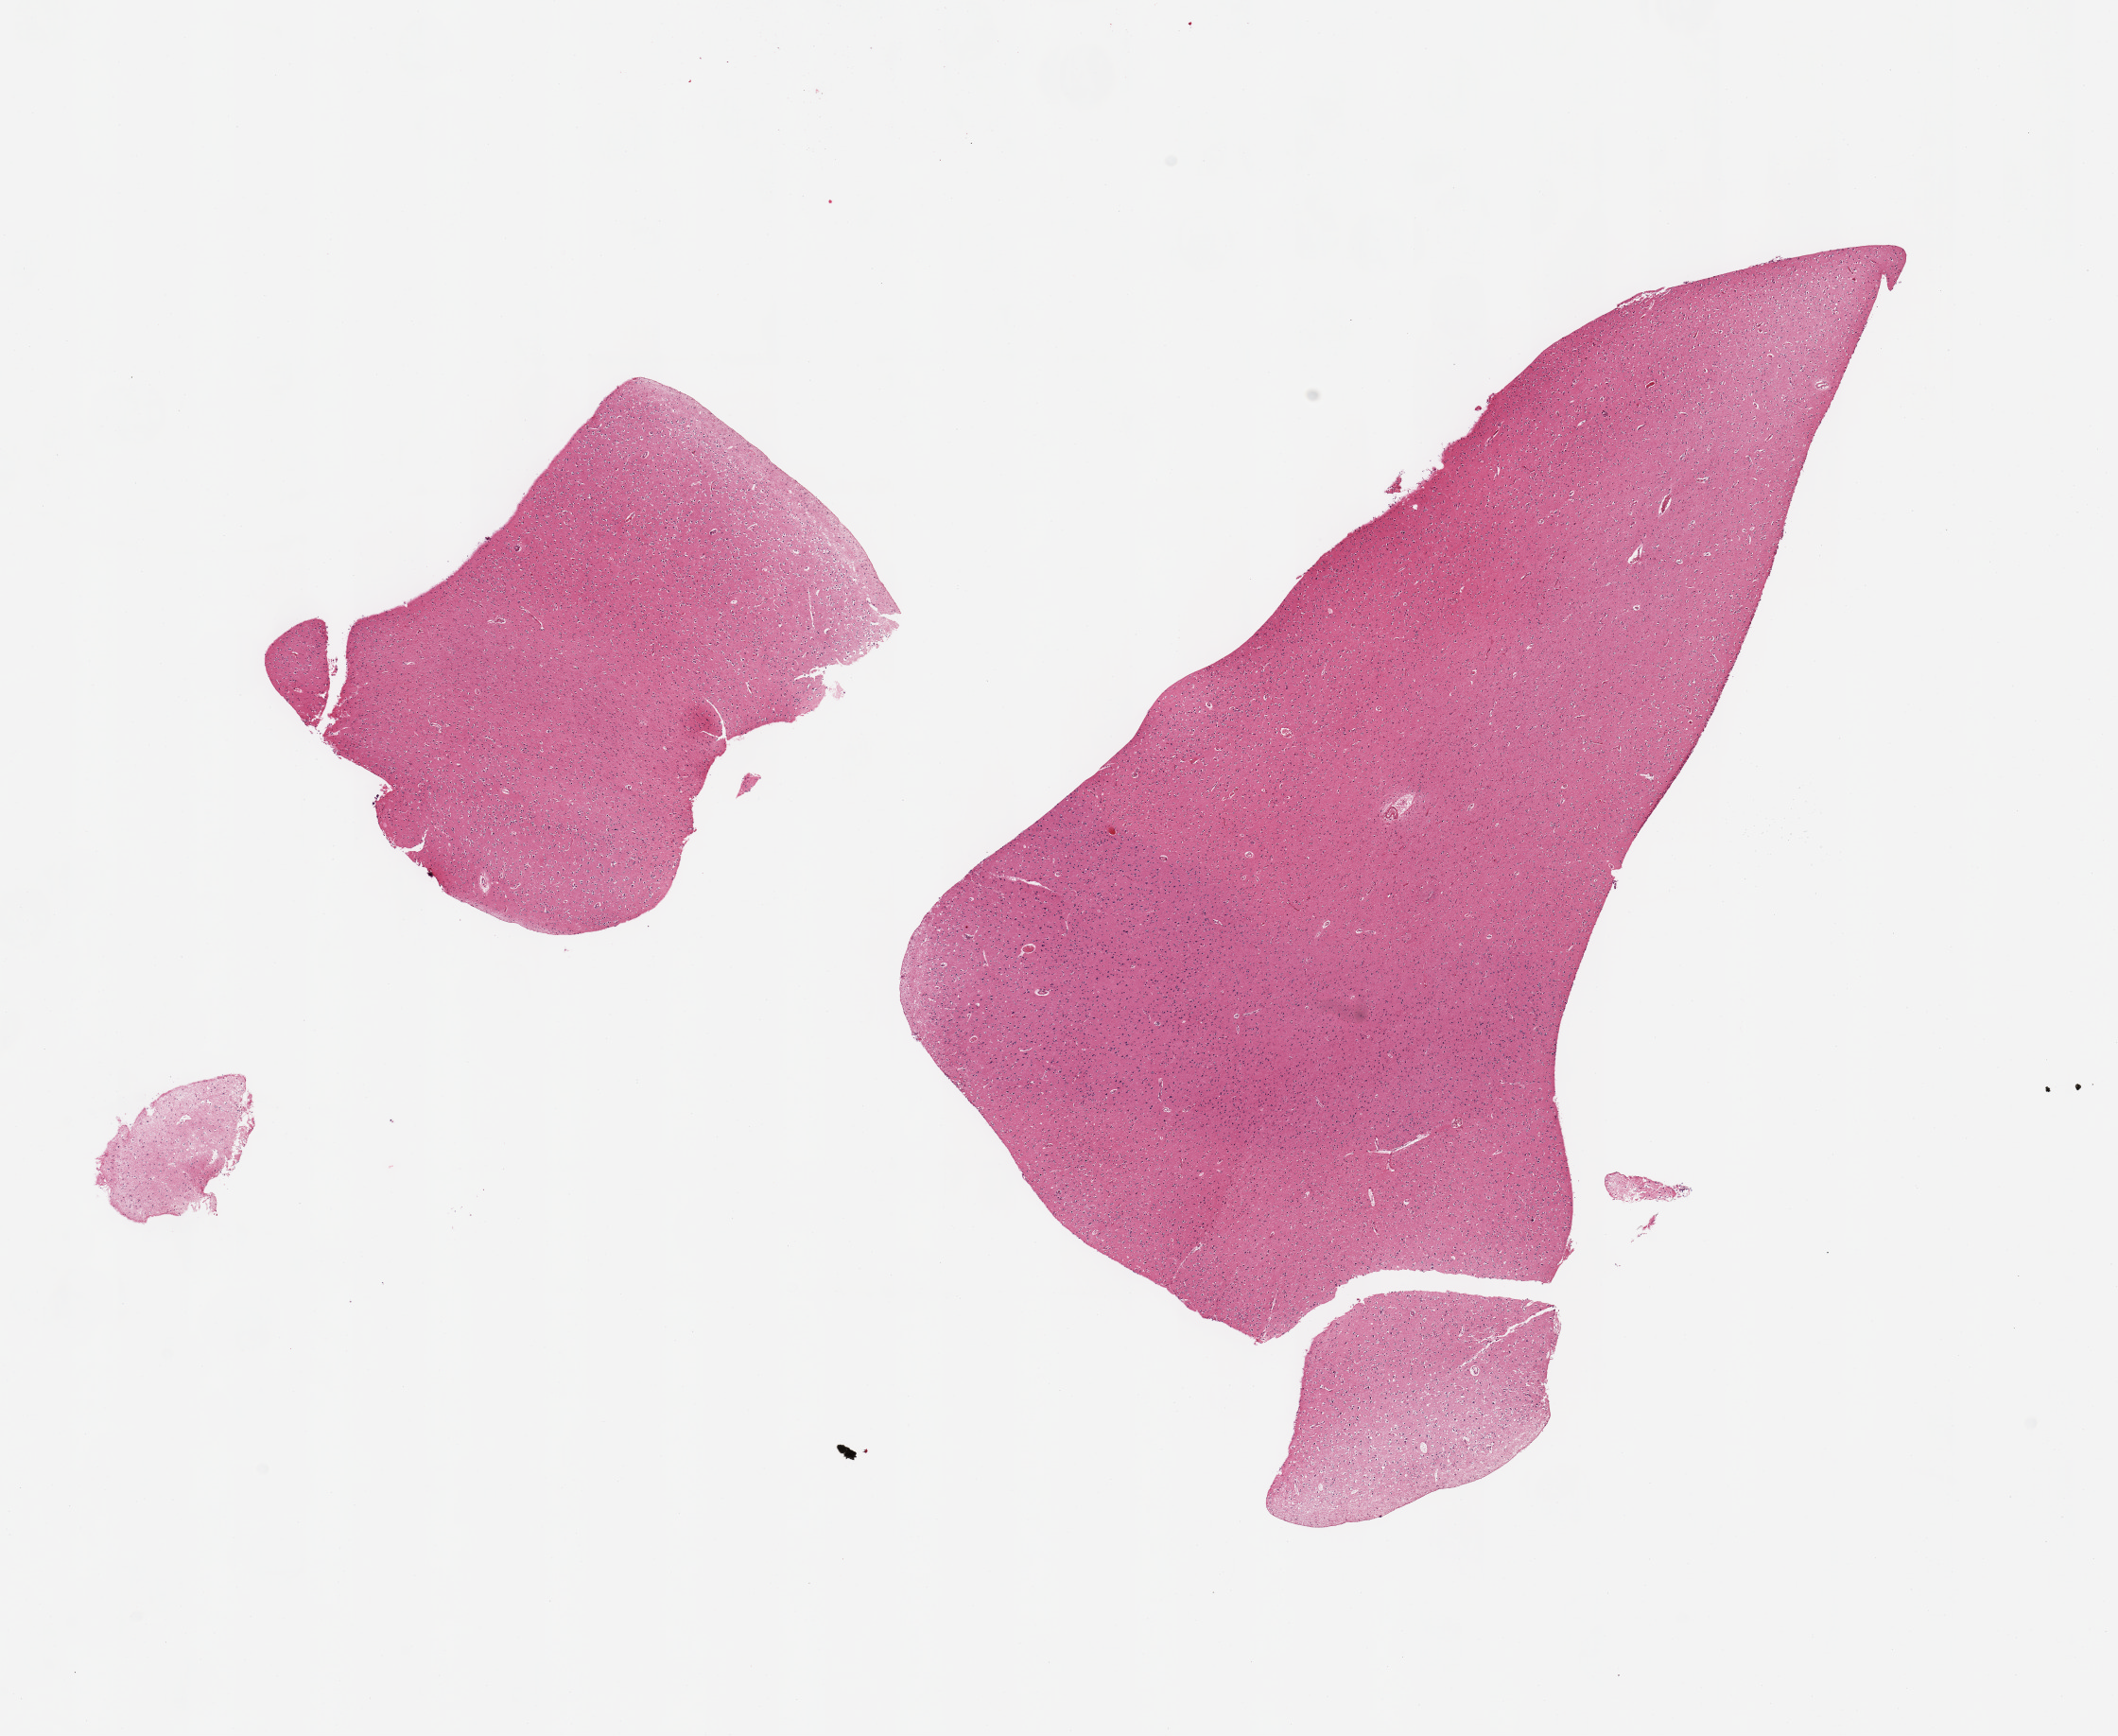
H&E whole-slide image, brightfield, low-resolution overview of the scanned area, about 17.7 x 14.5 mm, PAXgene-fixed paraffin-embedded (PFPE) section, target tissue: cerebral cortex, tissue donor sample. Male donor.
Pathologist's review note for this sample: 2 pieces.